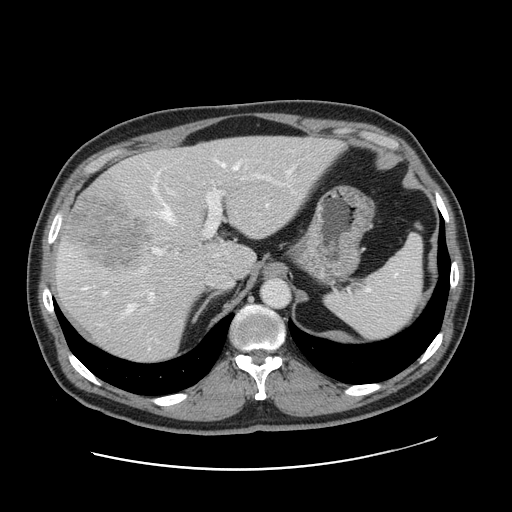
Contrast-enhanced abdominal CT, one axial slice; slice 116 of 178 in the series (ordered by position); 120 kVp; intravenous contrast given; soft-tissue window (W 400 / L 40 HU); 2.5 mm slice thickness; 512 × 512 image matrix, field of view 403 × 403 mm. Male patient, age 63 years. Case-level facts recorded for this patient, not image findings: diagnosis: colorectal cancer liver metastases, imaged before liver resection; multiple liver metastases: yes; largest metastasis: 8 cm; disease in both lobes: yes.
Structures marked on this image (outlined manually by an expert reader):
- hepatic veins: bounding box <83,163,291,312> (left, top, right, bottom; pixels)
- liver: <55,137,340,363>
- planned liver remnant (the part of the liver to remain after resection): <138,137,340,276>
- portal vein (with intrahepatic branches): <142,173,270,311>
- liver metastasis: <64,195,154,267>